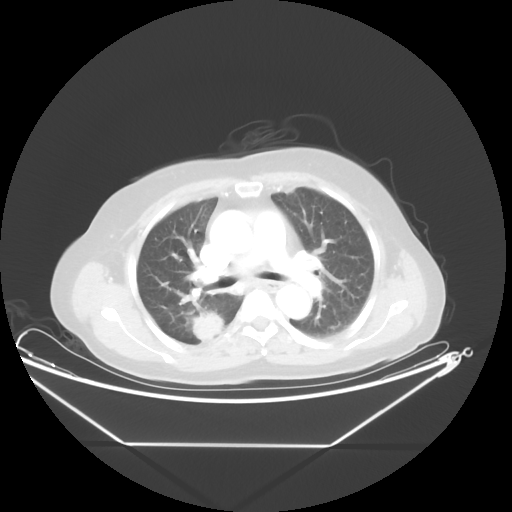
Chest CT, one axial slice. Slice 29 of 48 in the series (ordered by position). Reconstruction kernel STANDARD. Lung window (W 1500 / L -600 HU). 5 mm slice thickness. 512 × 512 image matrix. Female patient, age 62 years. From the clinical record (not read from this slice): clinical TNM (as recorded): T1c N0 M0.
Structures marked on this image (bounding box drawn by a radiologist):
- lung tumour (recorded histology: adenocarcinoma): bounding box [x1, y1, x2, y2] px = [179, 302, 239, 356]